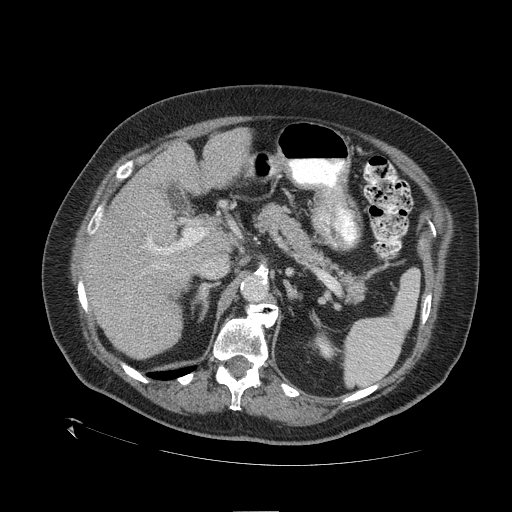
Contrast-enhanced abdominal CT (liver protocol), one axial slice; position 67 of 109 along the scan axis; reconstruction kernel STANDARD; one of 2 acquisitions stored at this slice position; soft-tissue window (W 400 / L 40 HU); 2.5 mm slice thickness; 512 × 512 image matrix. From the clinical record (not read from this slice): diagnosis: hepatocellular carcinoma (patient treated with transarterial chemoembolisation; whether this scan precedes or follows treatment is not stated here); TNM stage (as recorded): Stage-I; Child-Pugh class: A.
Outlined on this slice (semi-automatically segmented with operator editing):
- liver parenchyma outside the tumour (the mass and vessels are separate outlines, so this box may not span the whole liver): box from (x=84, y=128) to (x=250, y=358) px
- liver vessels: (x=91, y=214)–(x=205, y=269)